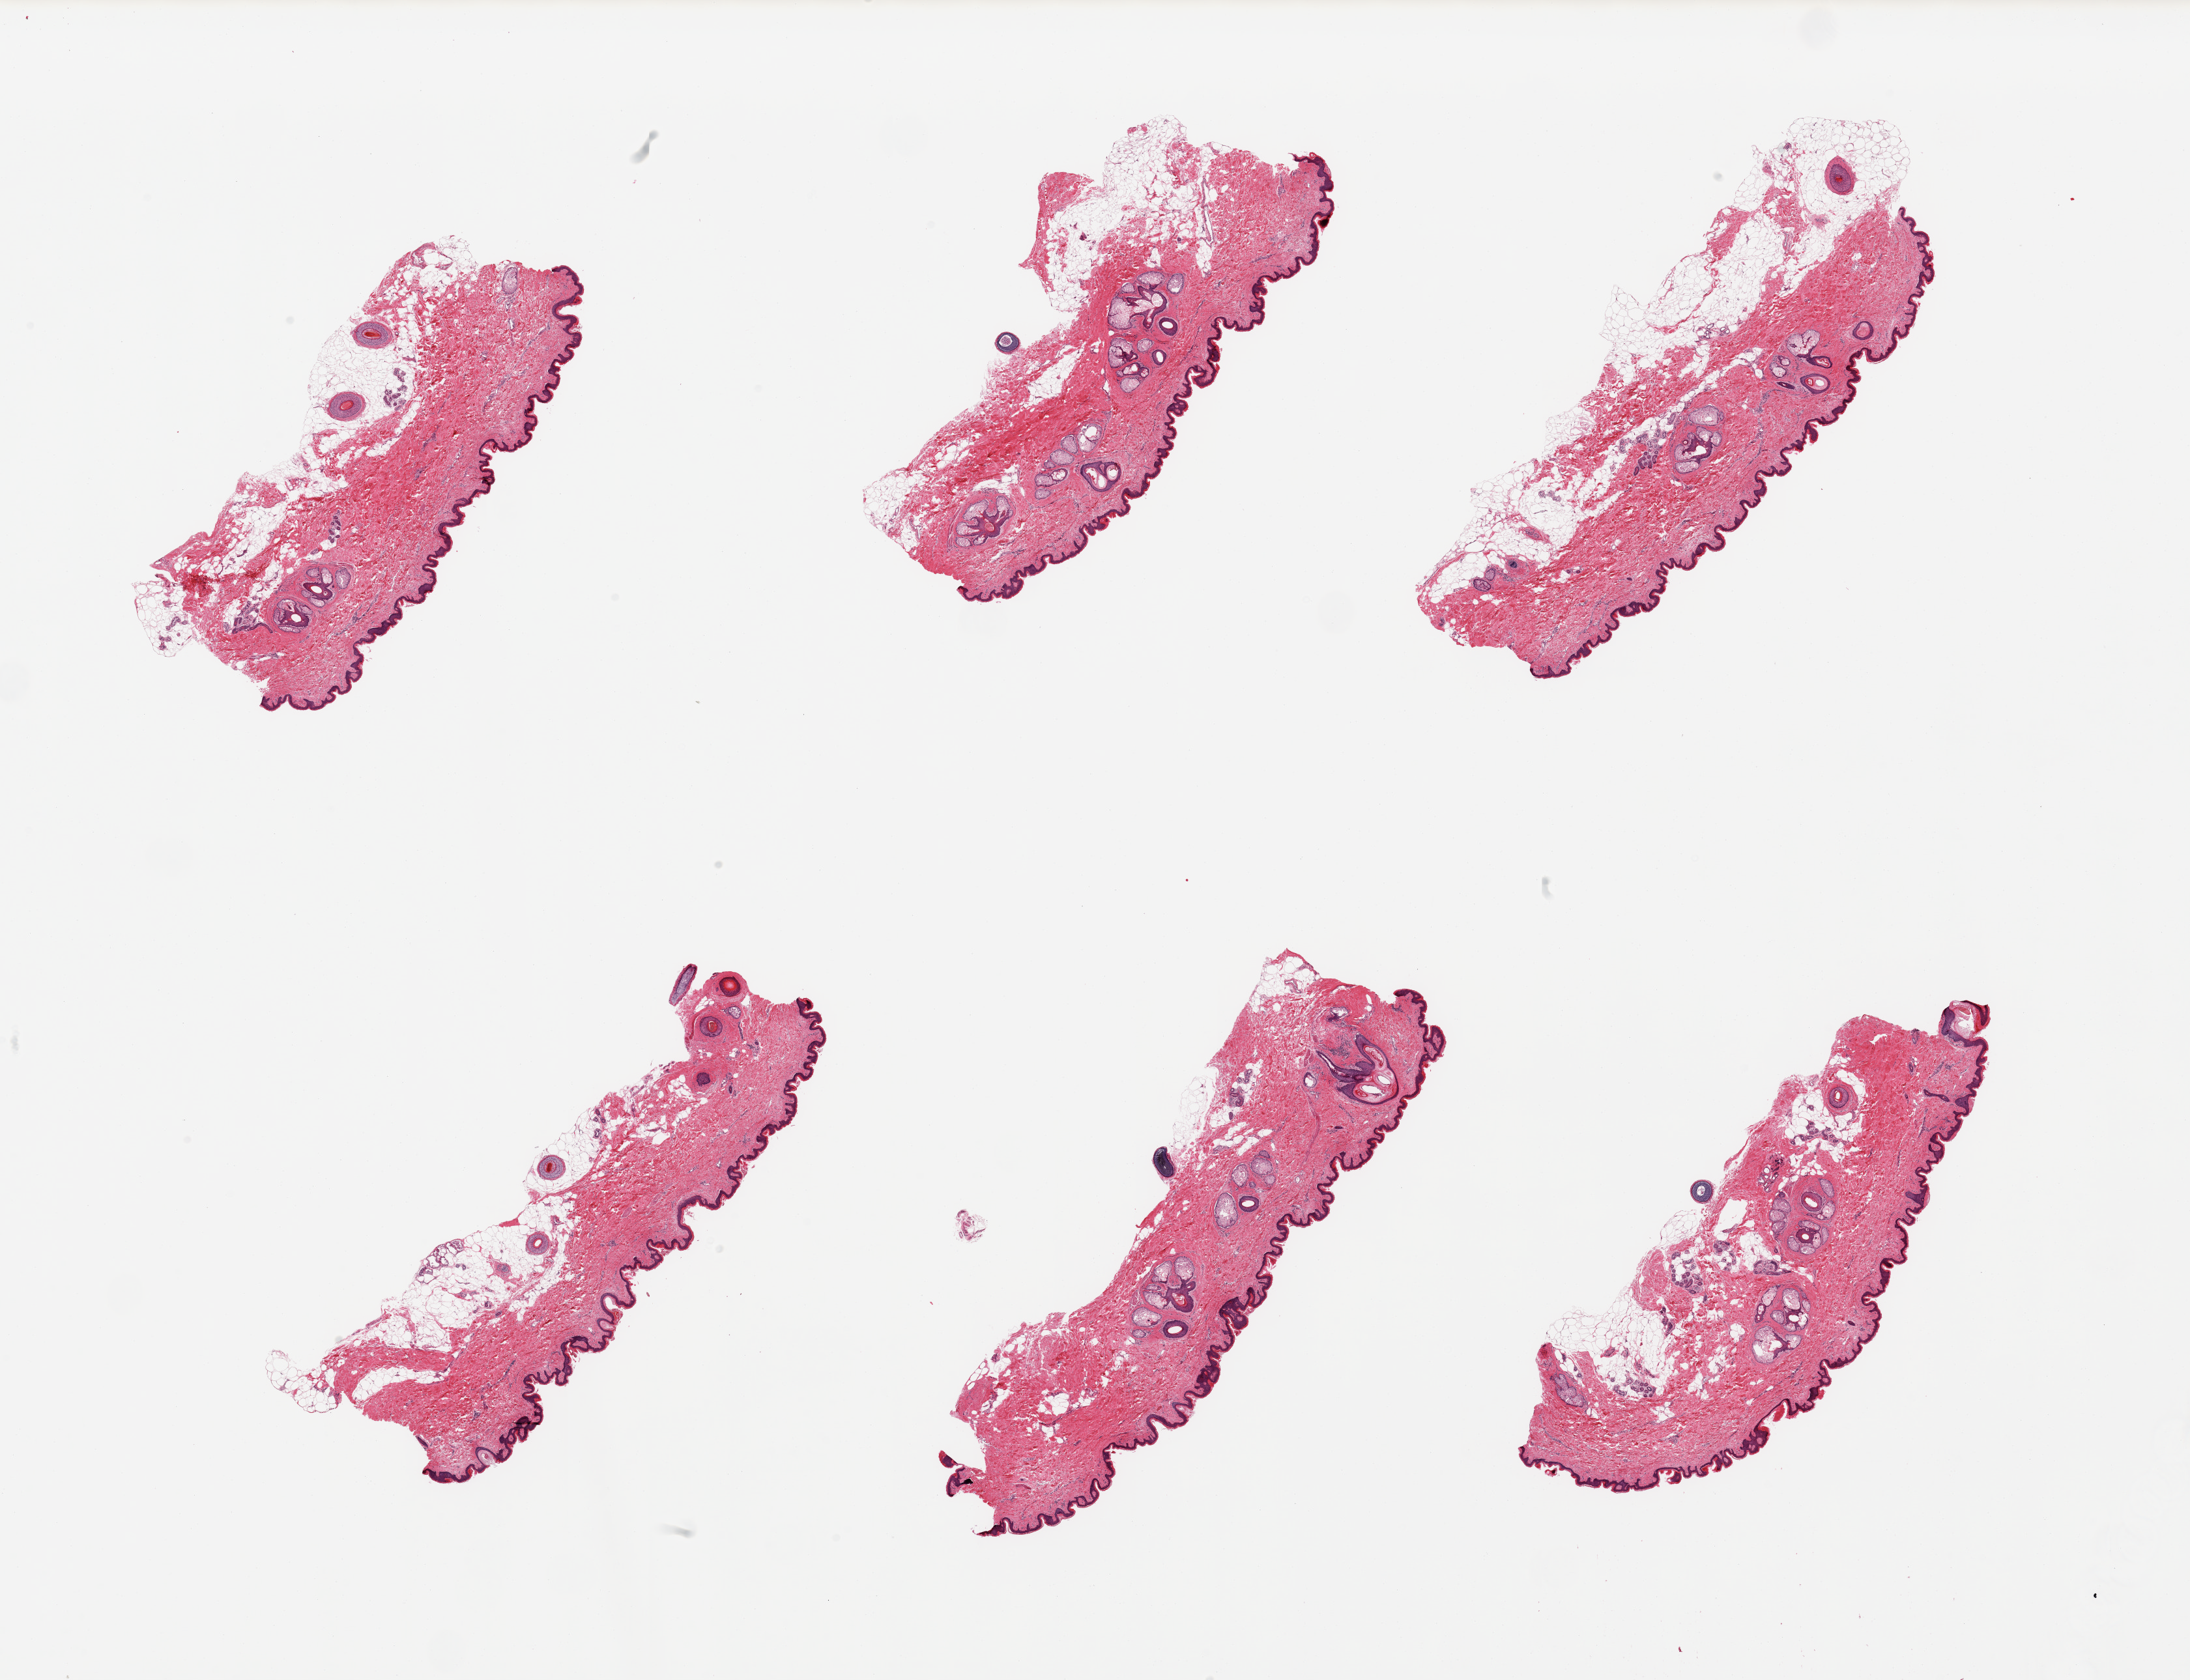
Haematoxylin and eosin whole-slide image, whole scanned area (about 26.6 x 20.4 mm) shown as a low-resolution overview. PAXgene-fixed, paraffin-embedded tissue. Section of skin of suprapubic region (target tissue). Donor tissue sample. Male donor.
Review note (as recorded): 6 pieces, squamous epithleium is ~40 microns, adherent dermal fat up to ~1mm.